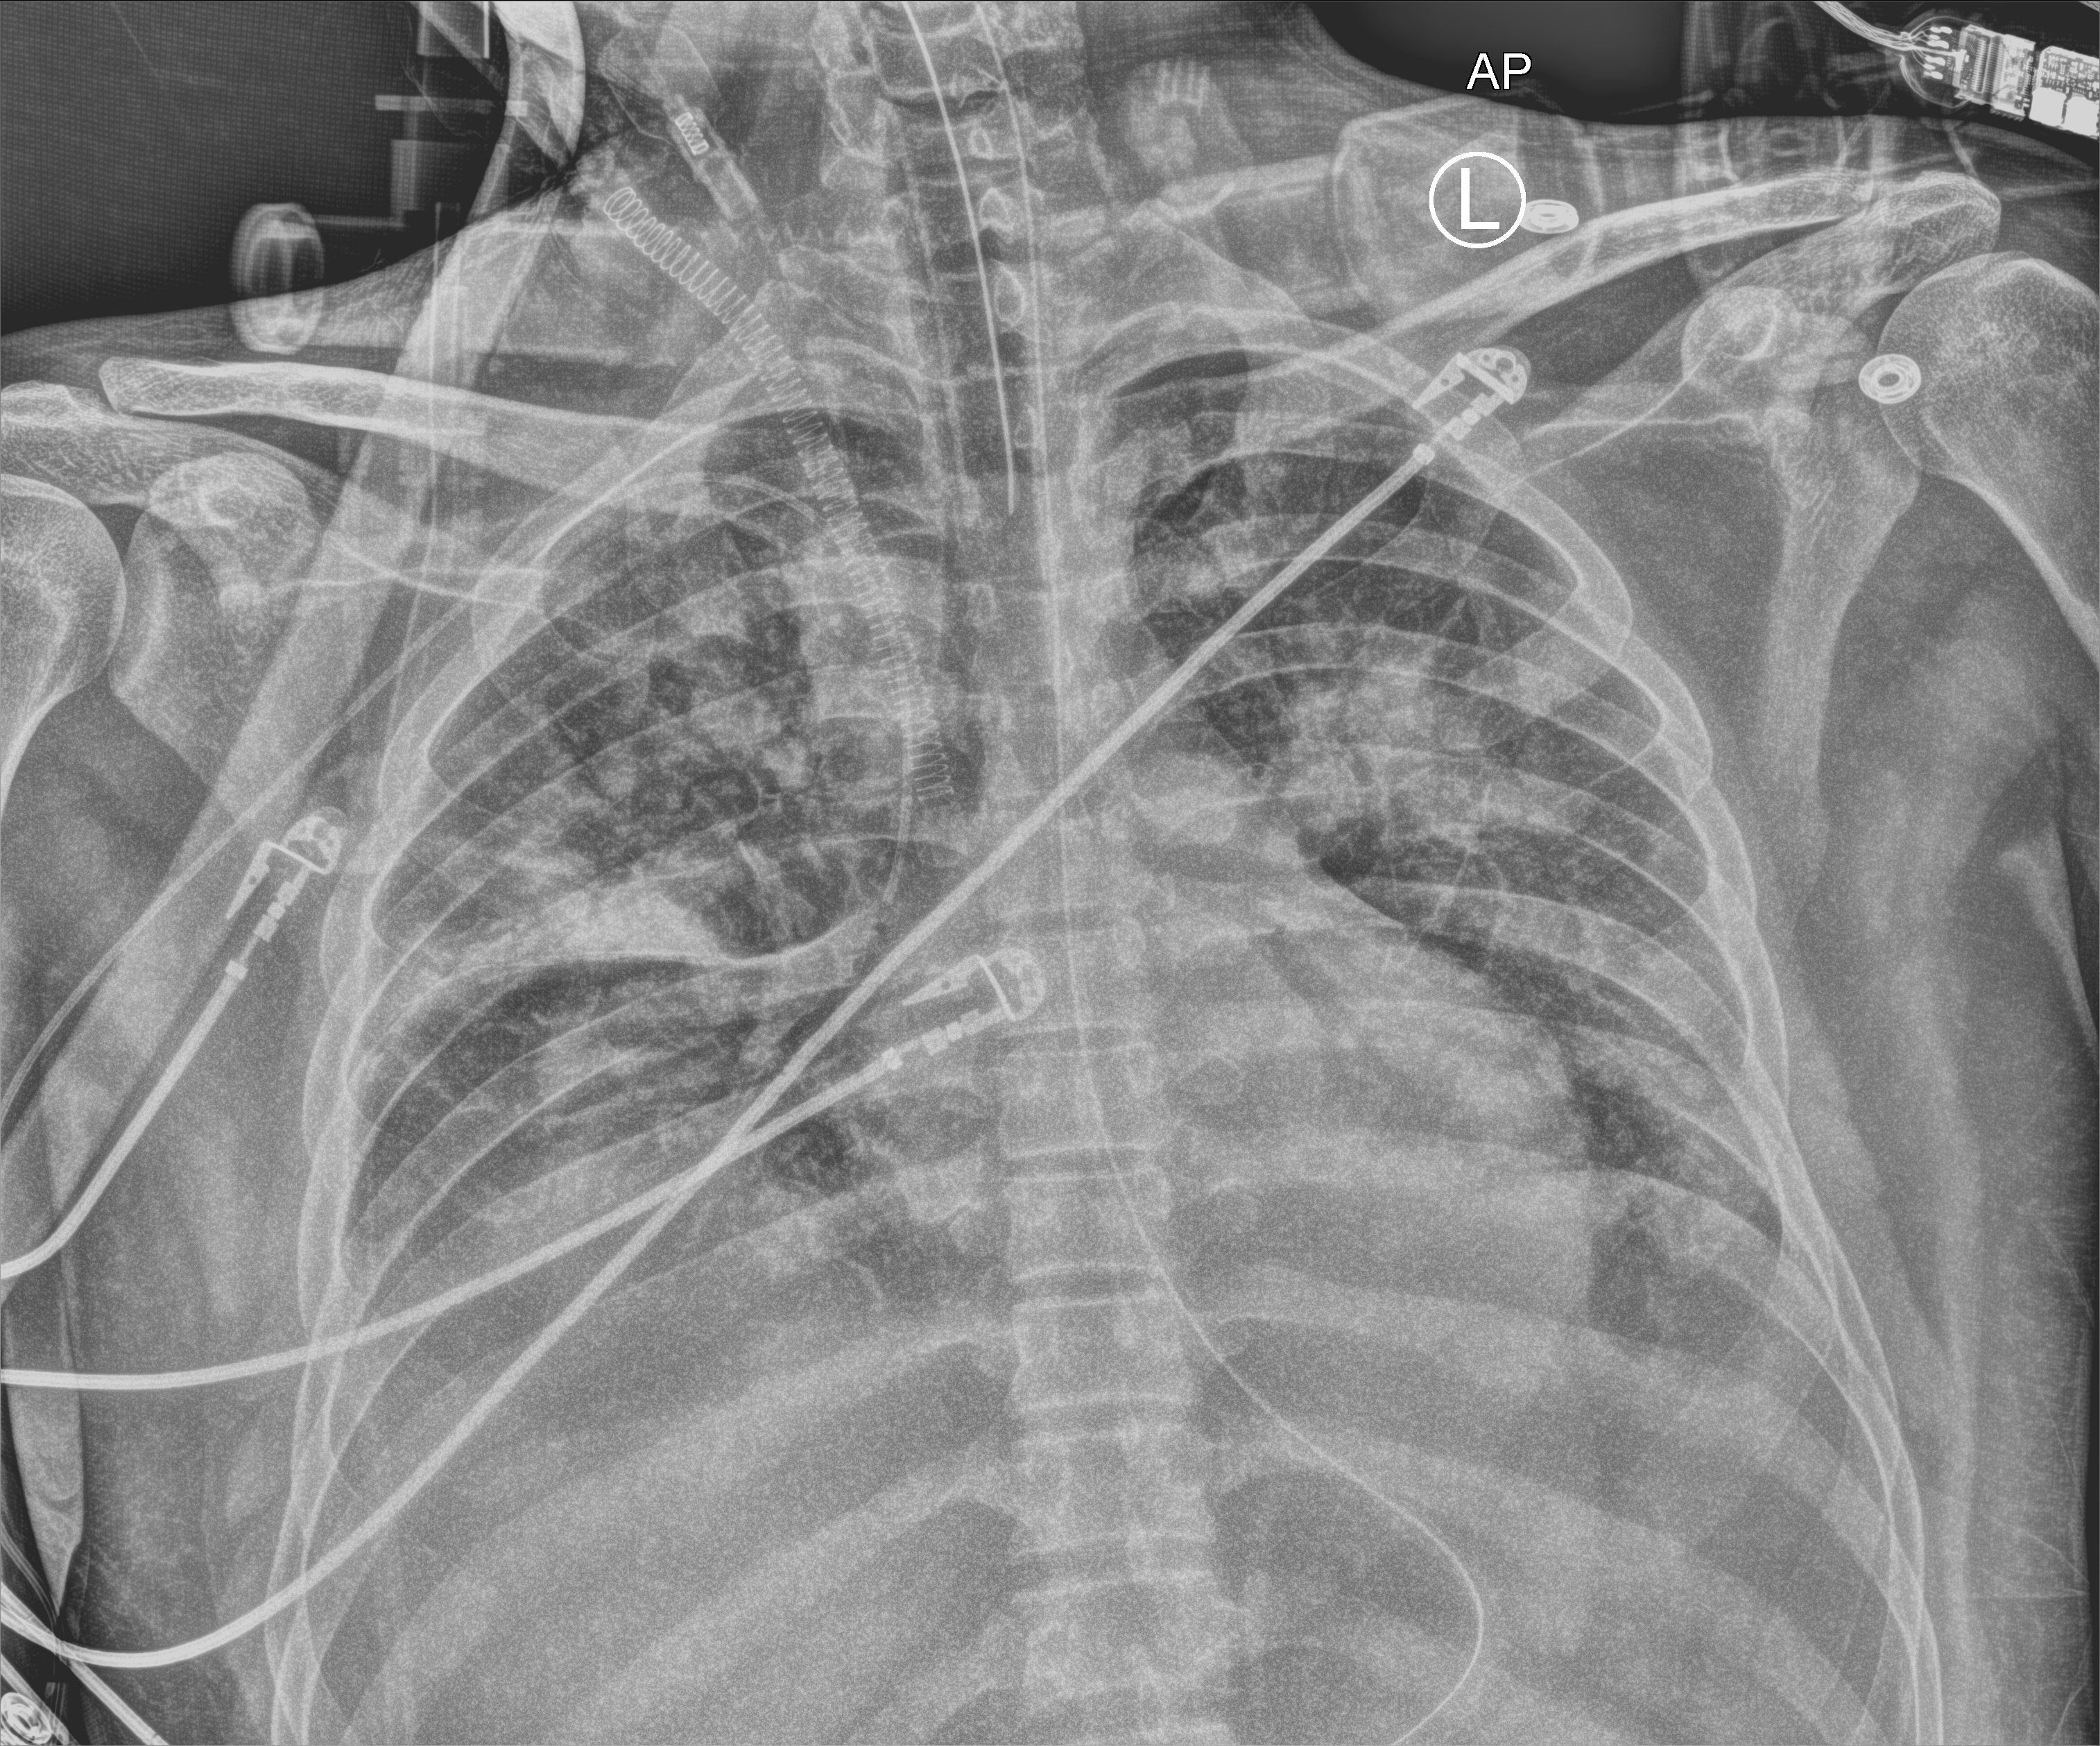
Portable chest radiograph; anteroposterior (AP) projection. Patient hospitalised with COVID-19, aged 18–59 years.
Admission-level facts for this patient (not findings on this image; timing relative to this image not recorded): length of hospital stay: 60 days; other chronic lung disease (admission record): no.